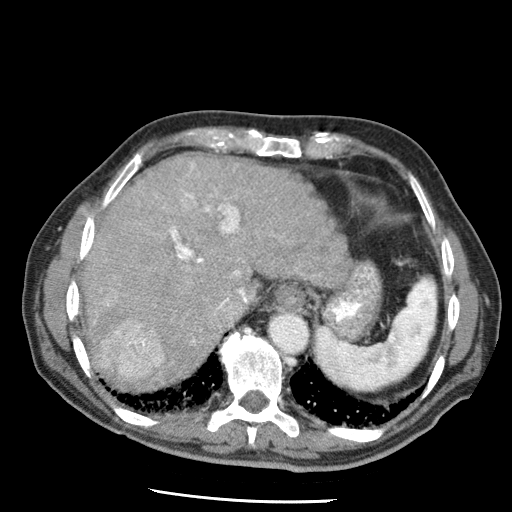
Contrast-enhanced abdominal CT (liver protocol), one axial slice. Slice 52 of 79 in the series (ordered by position). Reconstruction kernel STANDARD. 120 kVp. Soft-tissue window (W 400 / L 40 HU). 512 × 512 image matrix, field of view 320 × 320 mm. From the clinical record (not read from this slice): diagnosis: hepatocellular carcinoma (patient treated with transarterial chemoembolisation; whether this scan precedes or follows treatment is not stated here); TNM stage (as recorded): Stage-IIIA; Child-Pugh class: A; tumour differentiation: moderately differentiated.
Structures marked on this image (semi-automatic segmentation, software-assisted and operator-edited):
- abdominal aorta: box from (x=271, y=315) to (x=307, y=354) px
- liver parenchyma outside the tumour (the mass and vessels are separate outlines, so this box may not span the whole liver): (x=80, y=155)–(x=346, y=382)
- mass: (x=100, y=319)–(x=165, y=382)
- liver vessels: (x=107, y=163)–(x=240, y=344)